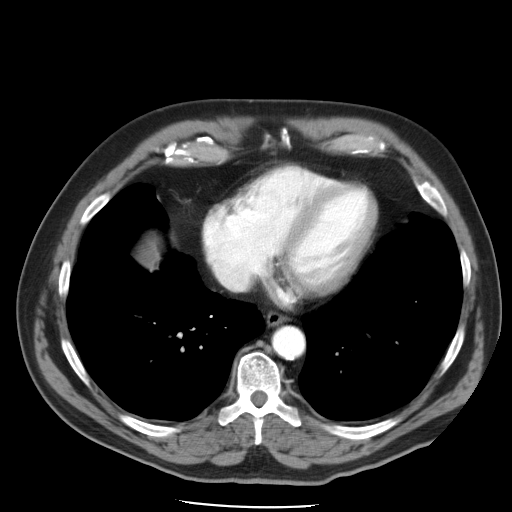
Contrast-enhanced abdominal CT, one axial slice. Slice 47 of 49 in the series (ordered by position). Reconstruction kernel STANDARD. 120 kVp. Intravenous contrast given. Soft-tissue window (W 400 / L 40 HU). 512 × 512 image matrix. Male patient, age 68 years. Case-level facts recorded for this patient, not image findings: diagnosis: colorectal cancer liver metastases, imaged before liver resection; multiple liver metastases: yes.
Annotated regions visible in this slice (manually delineated by an expert):
- hepatic veins: box from (x=211, y=261) to (x=253, y=290) px